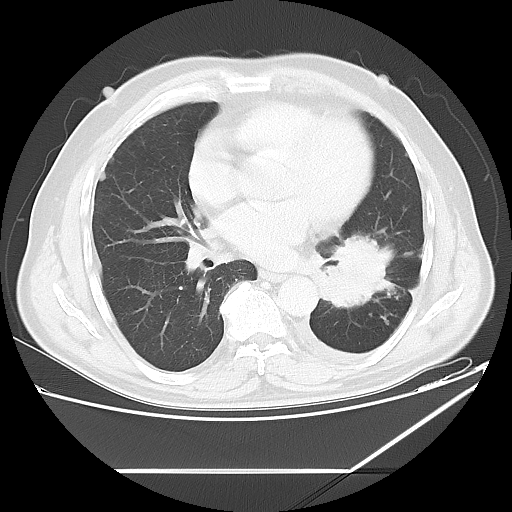
Chest CT, one axial slice. Position 28 of 60 along the scan axis. Reconstruction kernel LUNG. Lung window (W 1500 / L -600 HU). 5 mm slice thickness. 512 × 512 image matrix, field of view 395 × 395 mm. Patient: male, 62 years. From the clinical record (not read from this slice): clinical TNM (as recorded): T3 N0 M1.
Structures marked on this image (bounding box drawn by a radiologist):
- lung tumour (recorded histology: adenocarcinoma): bounding box [x1, y1, x2, y2] px = [316, 230, 395, 317]
- lung tumour (recorded histology: adenocarcinoma): [325, 232, 401, 318]